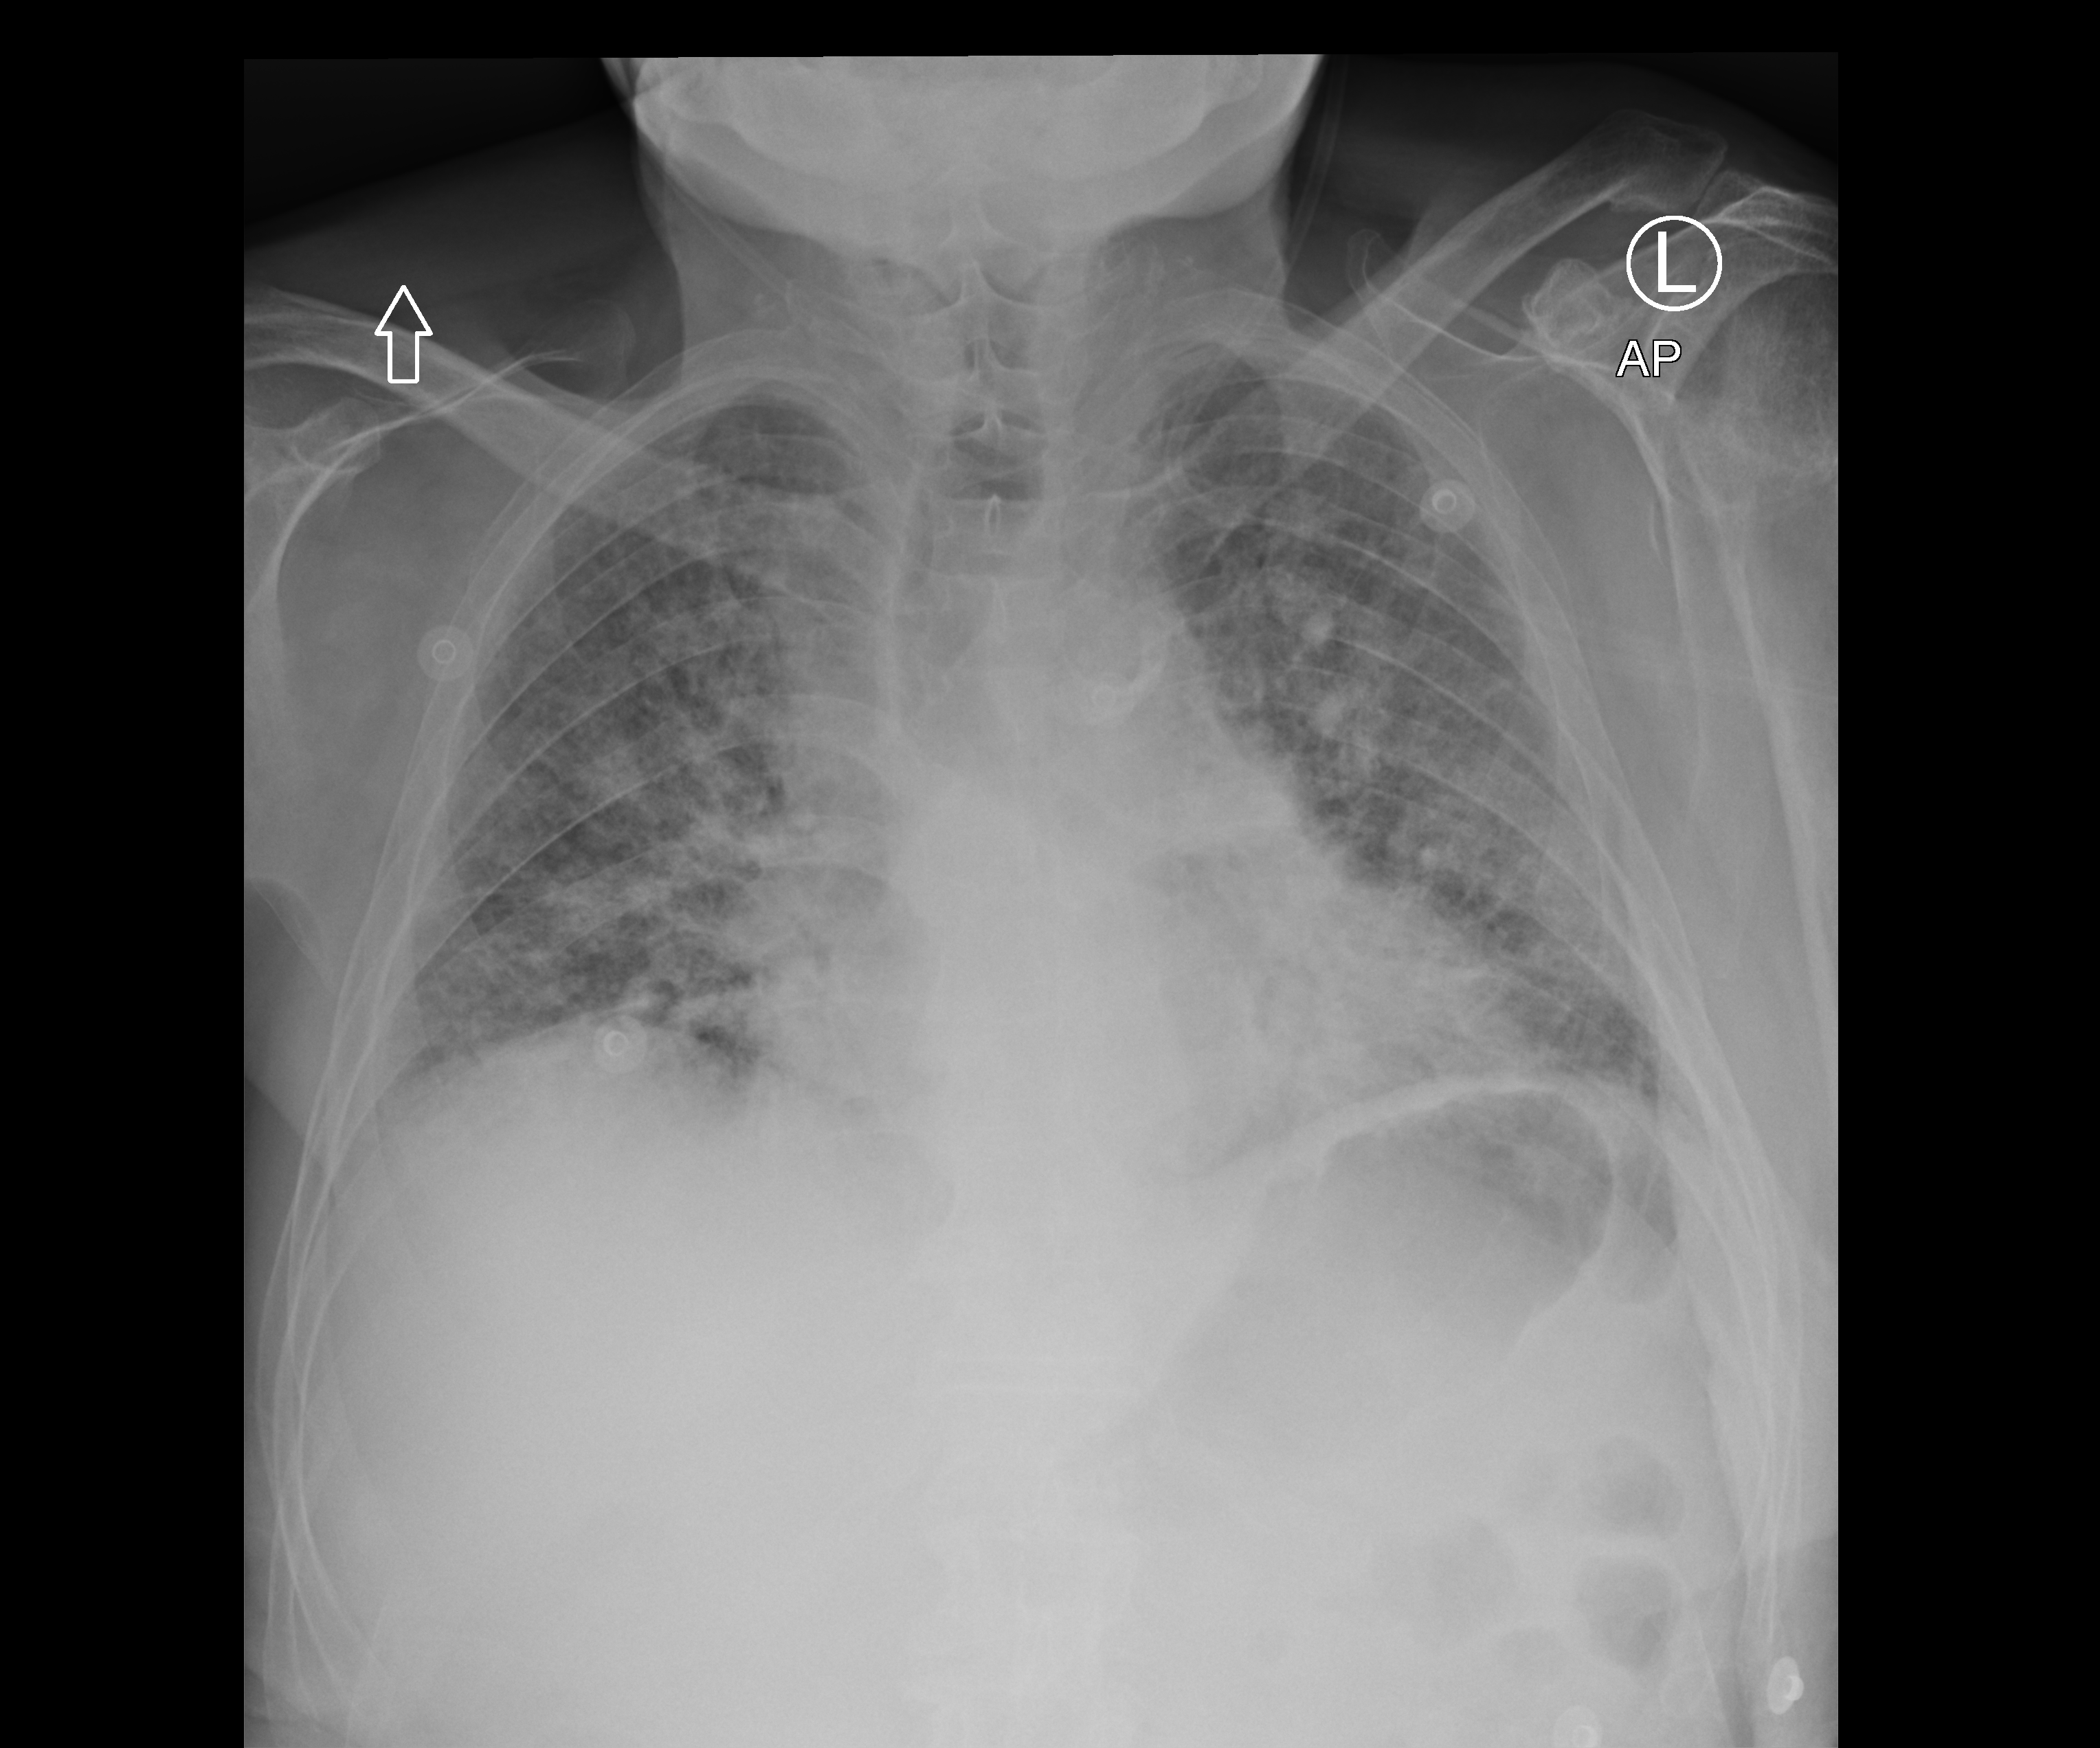
Chest radiograph (computed radiography); anteroposterior (AP) projection. Patient hospitalised with COVID-19; male, aged 60–74 years.
Hospital-stay facts (about this admission, not read from this image; timing relative to this image not recorded): admitted to intensive care during this hospital stay: no.